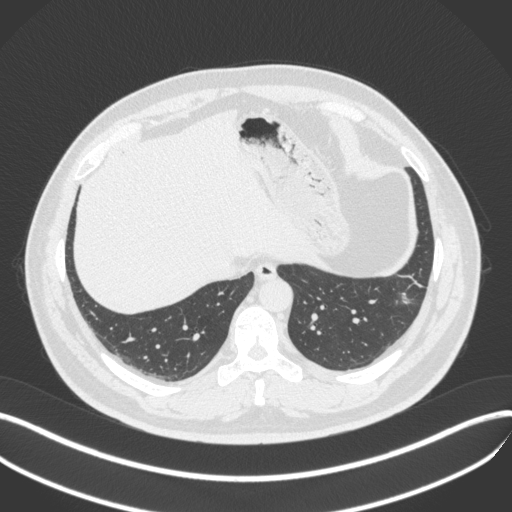
Chest CT, one axial slice. Reconstruction kernel B31f. 120 kVp. Lung window (W 1500 / L -600 HU). 1 mm slice thickness. 512 × 512 image matrix, field of view 400 × 400 mm. Male patient, age 39 years. Case-level facts recorded for this patient, not image findings: clinical TNM (as recorded): T2a N0 M0; histopathological grade: G2-3.
Outlined on this slice (rectangle marked by the reading radiologist):
- lung tumour (recorded histology: adenocarcinoma): box from (x=395, y=280) to (x=419, y=311) px